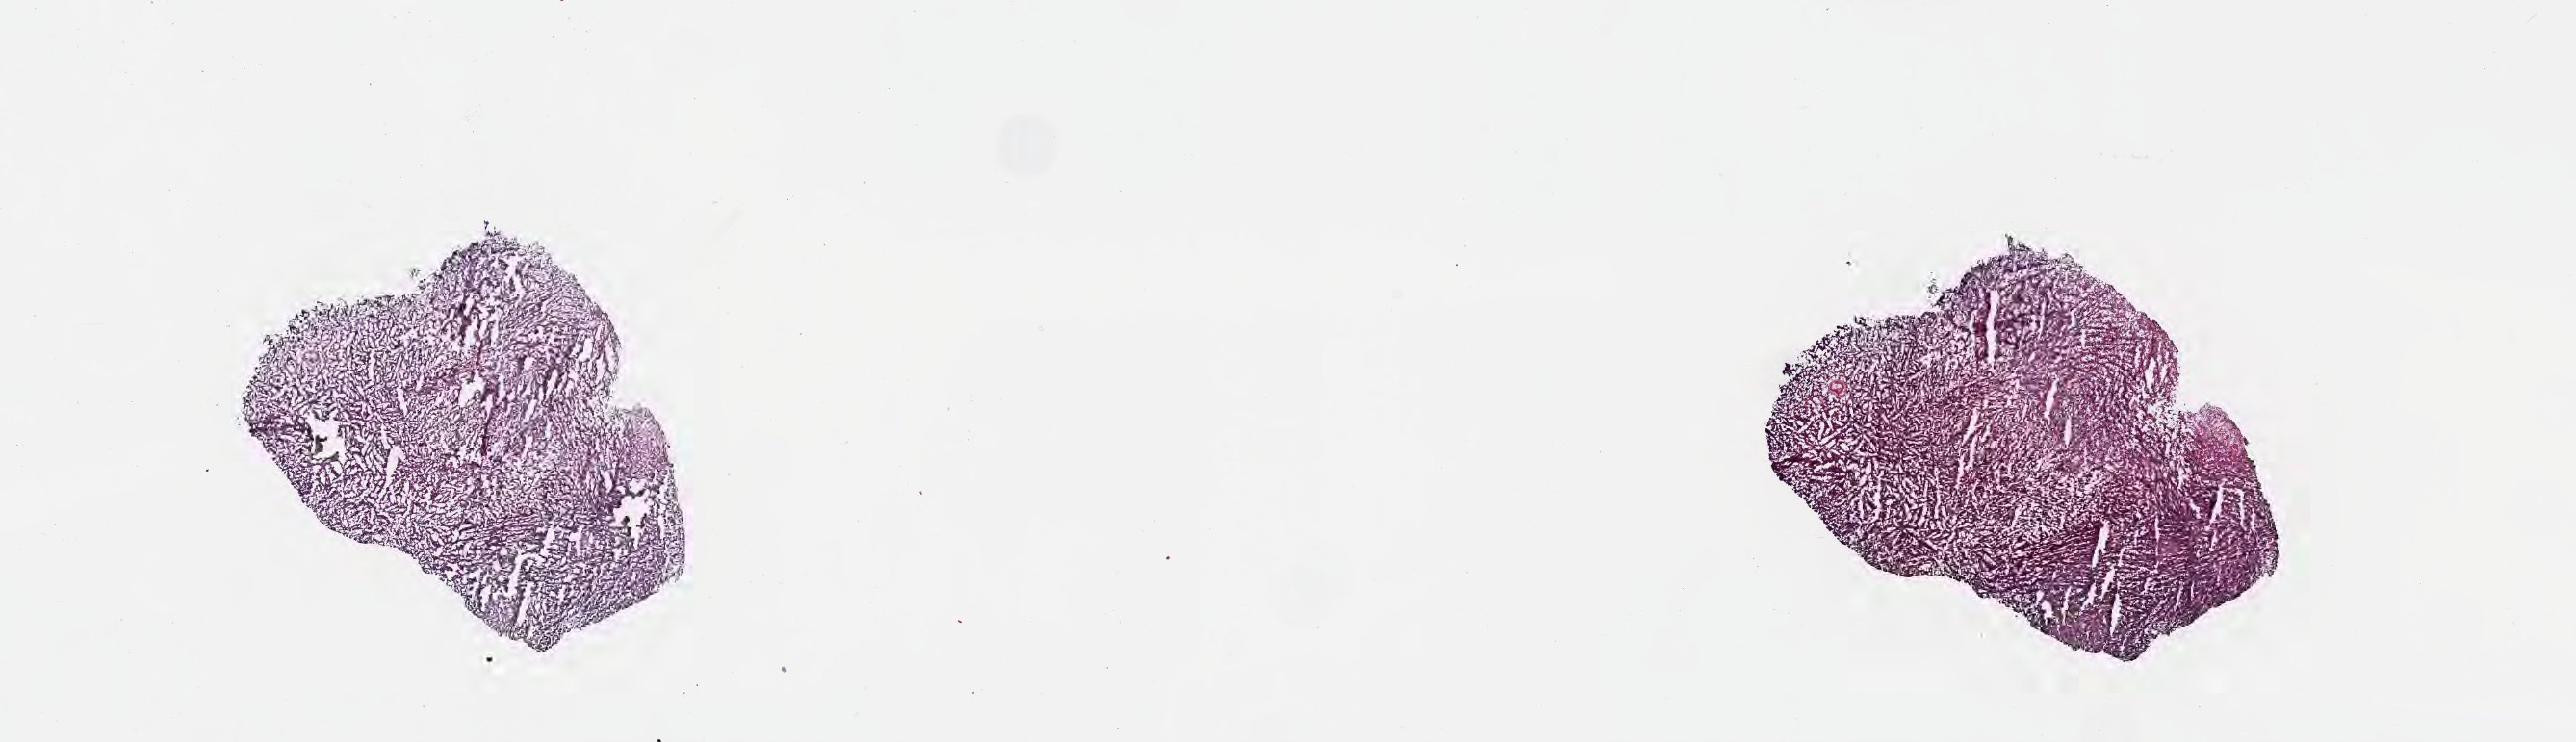
Haematoxylin and eosin whole-slide image — a low-resolution overview of the entire scanned area, about 21.6 x 6.2 mm; frozen section; specimen: primary tumor; anatomic site: mouth. Patient: male, age at initial diagnosis 9 years. Pathologist review of this section (percent, as recorded): tumor cells 90%, tumor nuclei 90%, stromal cells 5%, necrosis 5%, normal cells 0%. Infiltration values recorded for this section: lymphocyte infiltration 50%, monocyte infiltration 25%, neutrophil infiltration 5%.
Ann Arbor stage (patient): Stage IV. Histologic diagnosis: Burkitt lymphoma, NOS.